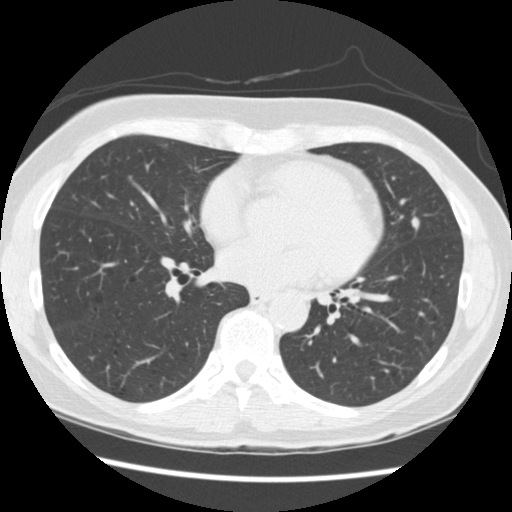
Low-dose screening chest CT, axial slice; third screening round (two years after baseline); lung window (W 1500 / L -600 HU); 2.5 mm slice thickness; standard (soft-tissue) reconstruction kernel (STANDARD); 120 kVp. Female participant, aged 60 years at enrolment. Current smoker at enrolment.
Expert-annotated lung lesion, bounding box <393,206,435,248> (left, top, right, bottom; pixels). Screening reader's record for this exam (one nodule recorded; not confirmed to be the boxed lesion): non-calcified nodule or mass ≥4 mm, lingula, 6 × 5 mm, smooth margins, soft tissue attenuation, pre-existing on the prior screen: yes; interval growth: yes. Official screen result: positive, other. Lung cancer was diagnosed 209 days after this screen: adenocarcinoma, NOS, lingula, poorly differentiated (G3), stage IA (AJCC 6th edition), 6 mm at pathology.